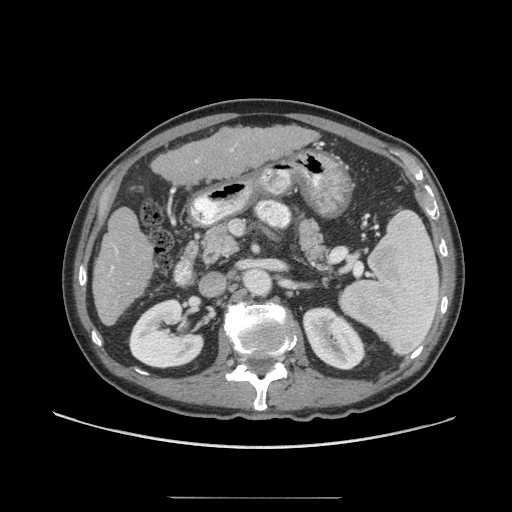
Contrast-enhanced abdominal CT (liver protocol), one axial slice. Position 25 of 71 along the scan axis. Reconstruction kernel STANDARD. 140 kVp. Soft-tissue window (W 400 / L 40 HU). 2.5 mm slice thickness. 512 × 512 image matrix, field of view 400 × 400 mm. Case-level facts recorded for this patient, not image findings: diagnosis: hepatocellular carcinoma (patient treated with transarterial chemoembolisation; whether this scan precedes or follows treatment is not stated here); TNM stage (as recorded): Stage-I; Child-Pugh class: A; tumour differentiation: well differentiated; tumour size: 3.5 cm.
Outlined on this slice (semi-automatically segmented with operator editing):
- liver parenchyma outside the tumour (the mass and vessels are separate outlines, so this box may not span the whole liver): box from (x=92, y=126) to (x=314, y=325) px
- liver vessels: (x=108, y=148)–(x=234, y=284)